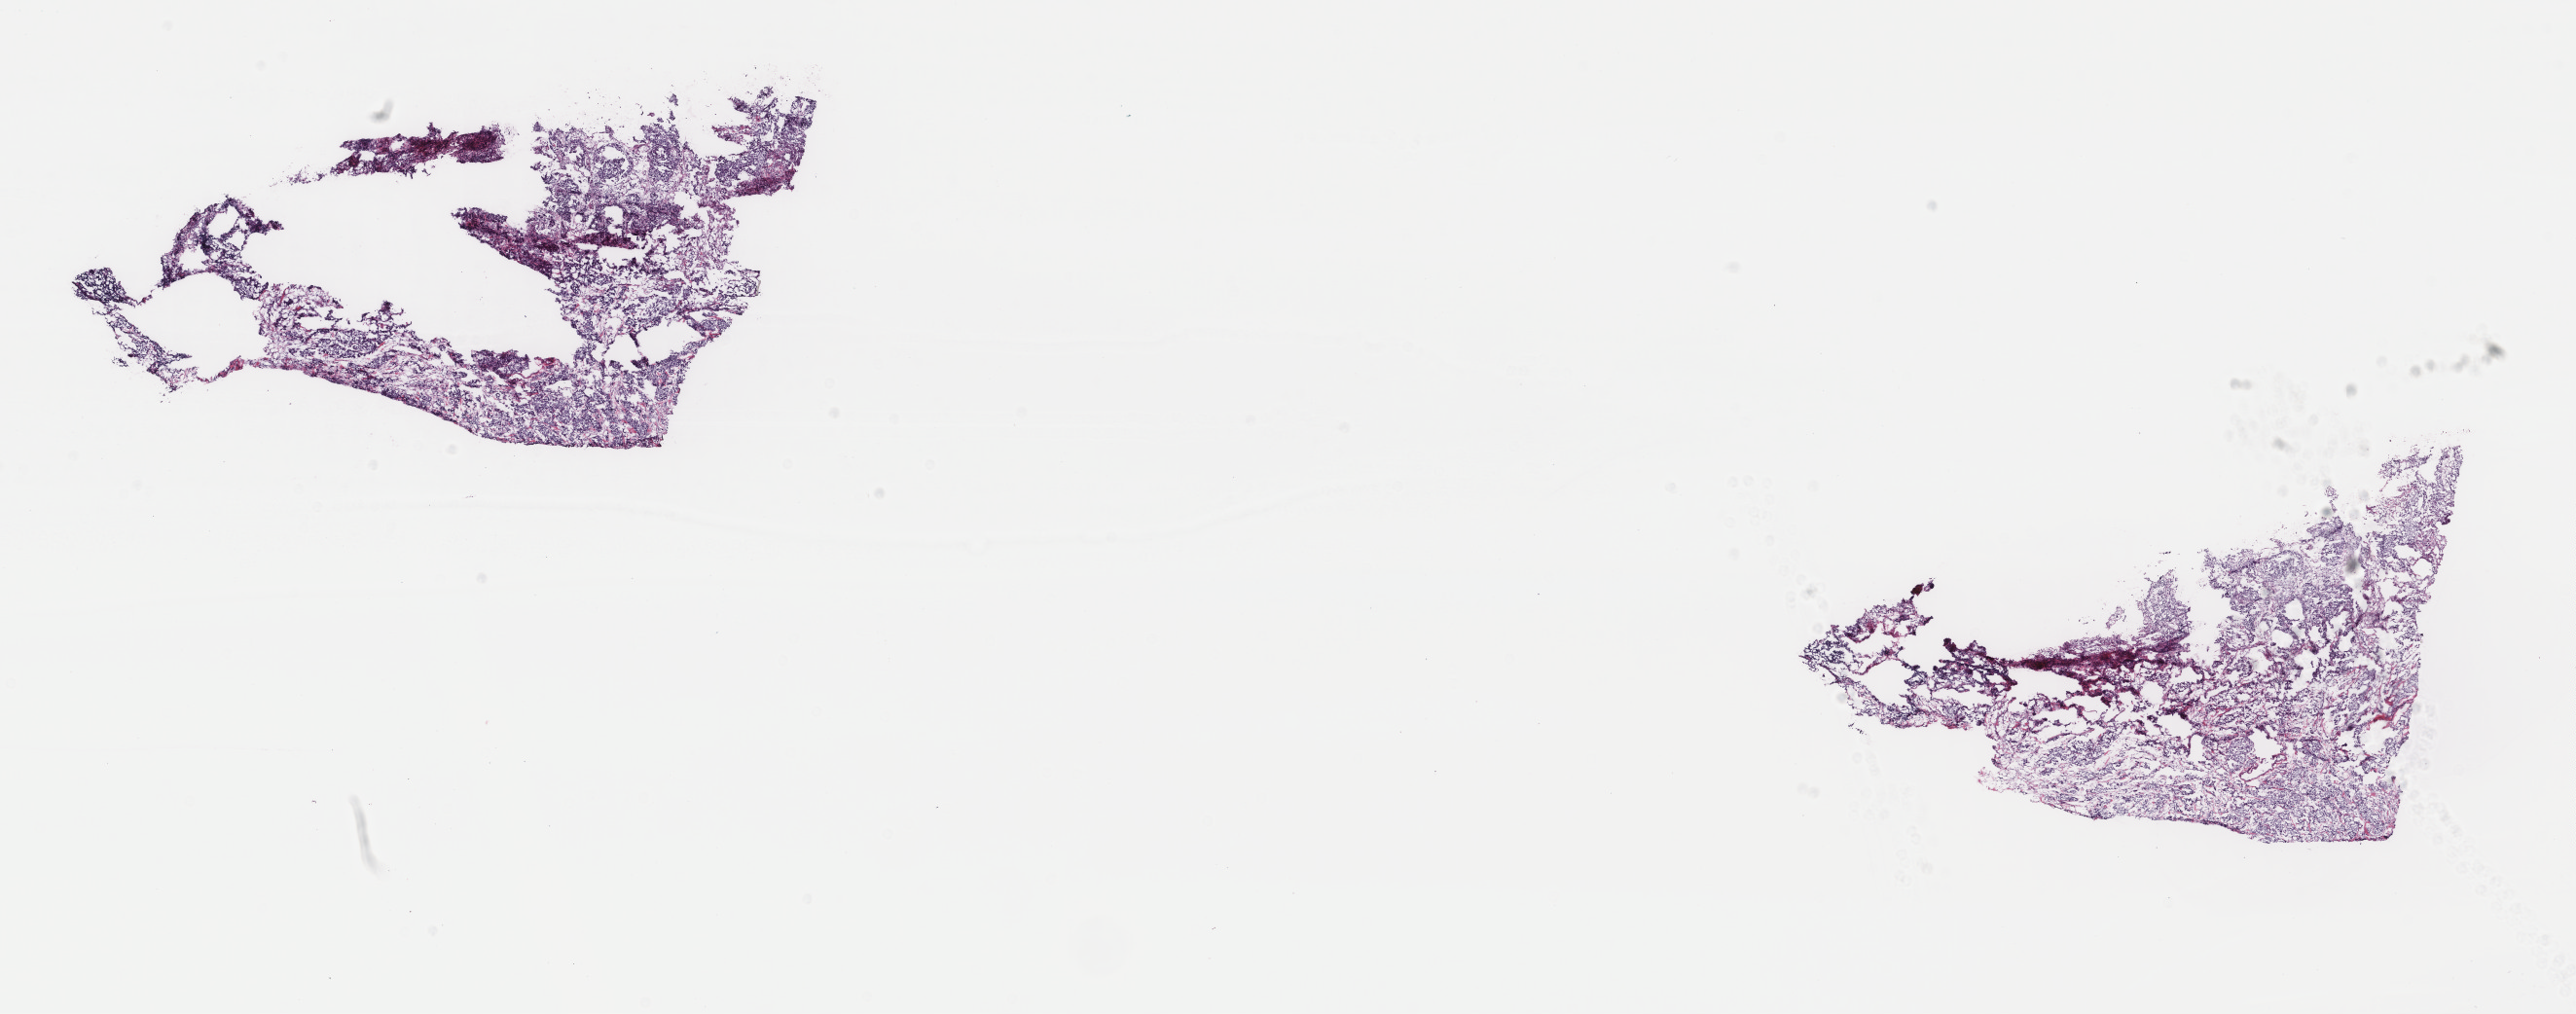
Whole-slide histology image, H&E-stained — low-resolution overview of the scanned area, about 21.0 x 8.3 mm. Frozen section from the top of the tissue portion. Primary tumour sample from the bladder. Patient: female, age at initial diagnosis 73 years. Histologic grade: high grade. Composition of this section per pathologist review: tumour cells 70%, tumour nuclei 80%, normal cells 0%, stromal cells 30%, necrosis 0%. Inflammatory infiltration, as recorded: lymphocyte infiltration 0%, monocyte infiltration 0%, neutrophil infiltration 0%.
Diagnosis: Transitional cell carcinoma (dome of bladder). AJCC pathologic stage: III.